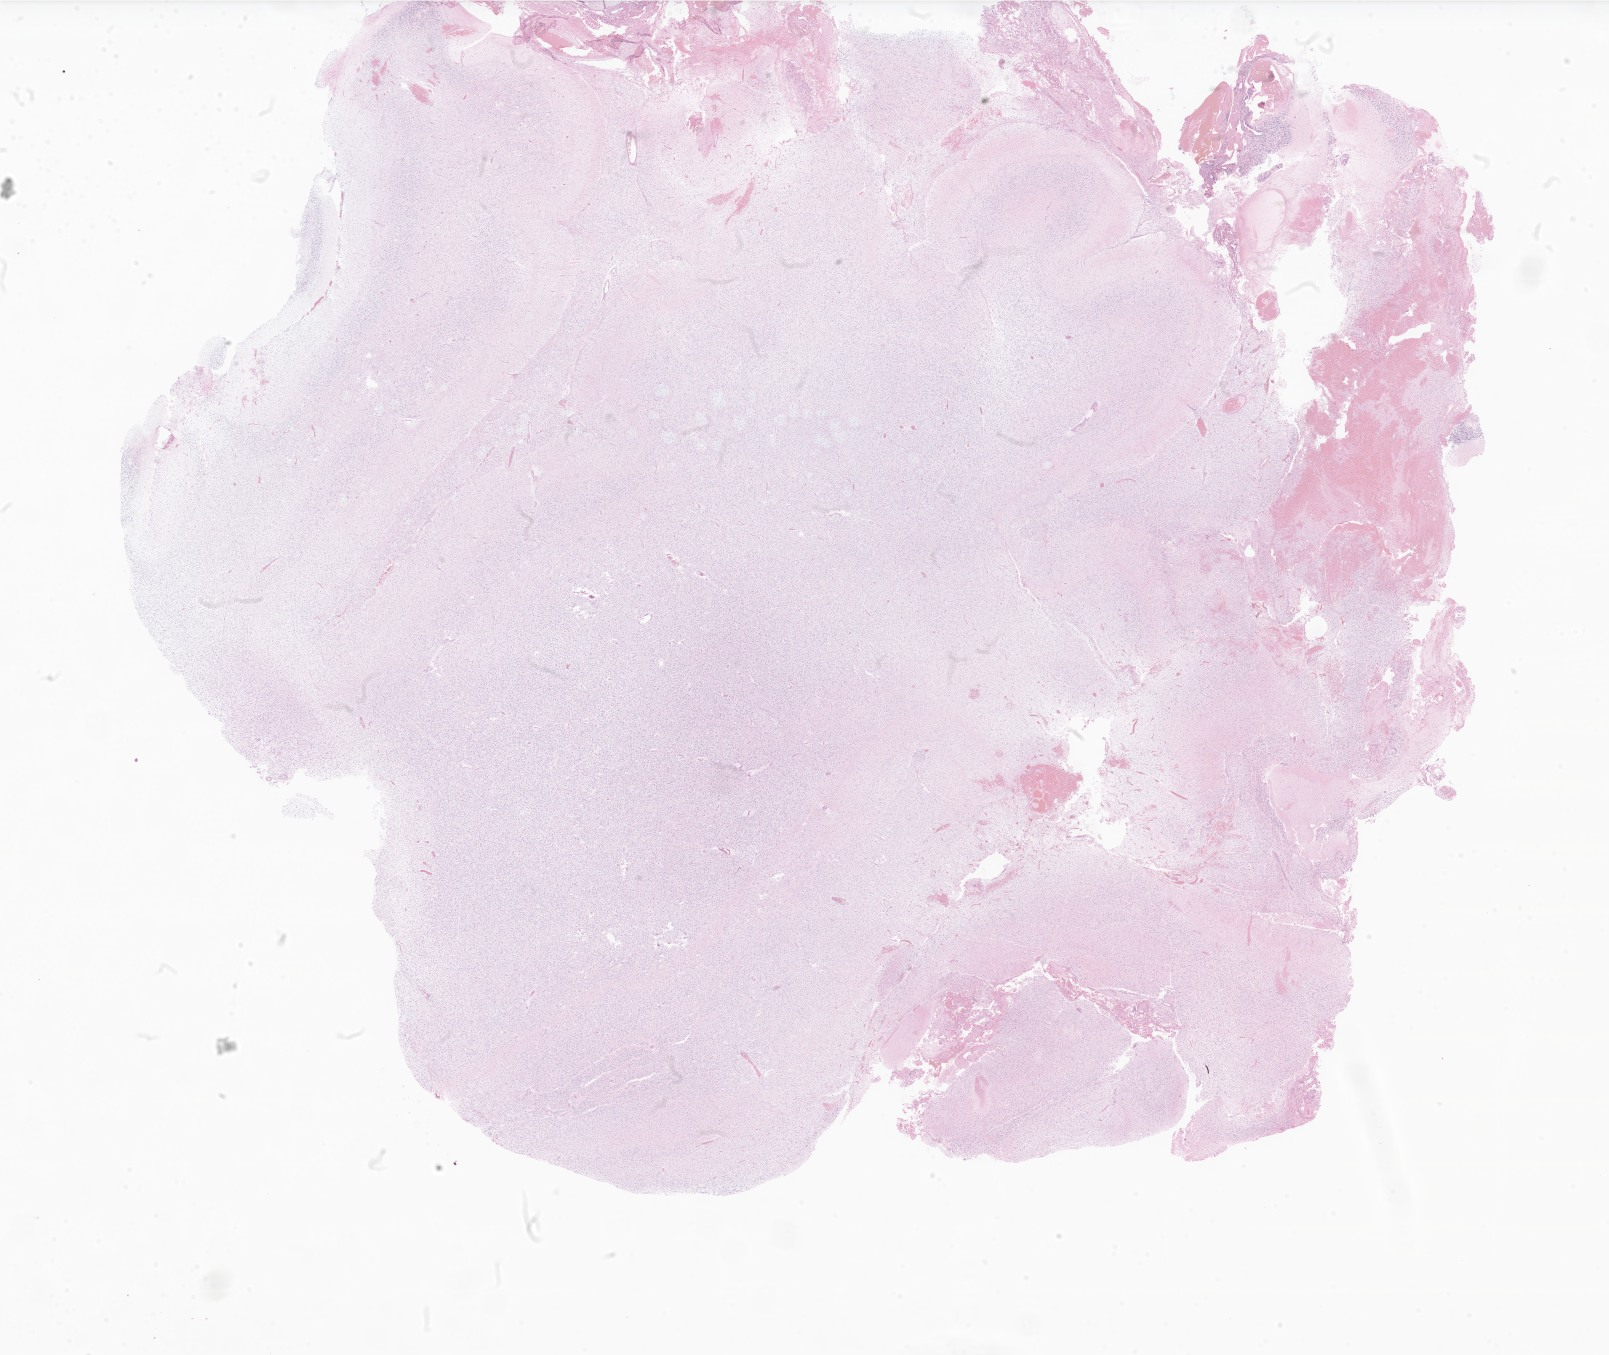
Whole-slide image, haematoxylin and eosin stain of tumor tissue from the brain — whole scanned area (about 27.1 x 22.9 mm) shown as a low-resolution overview. FFPE section. Female patient, age 180 months (15 years).
Diagnosis: Pilocytic astrocytoma.